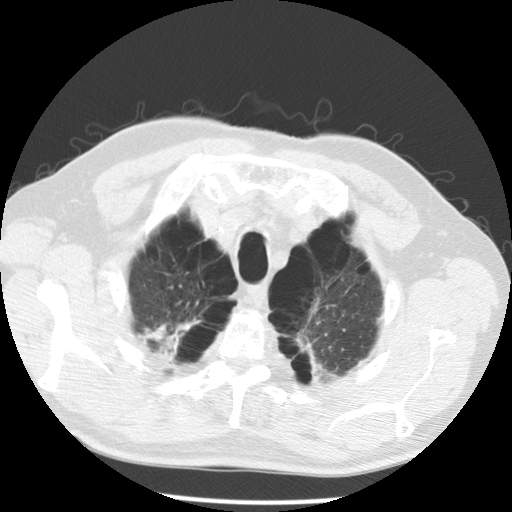
Low-dose screening chest CT, axial slice, second annual screen, lung window (W 1500 / L -600 HU), 2.5 mm slice thickness, 512 × 512 image matrix. Male, age 68 years at enrolment. Former smoker at enrolment.
Expert reader's lesion annotation, box from (x=128, y=297) to (x=202, y=370) px. The screening reader recorded 2 non-calcified nodules or masses ≥4 mm on this exam (lingula, left lower lobe); which of them this box marks is not recorded. Official screen result: positive, no significant change: stable abnormalities potentially related to lung cancer, unchanged since the prior screening exam. Lung cancer was diagnosed 617 days after this screen: large cell carcinoma, NOS, right upper lobe, poorly differentiated (G3), stage IV (AJCC 6th edition).